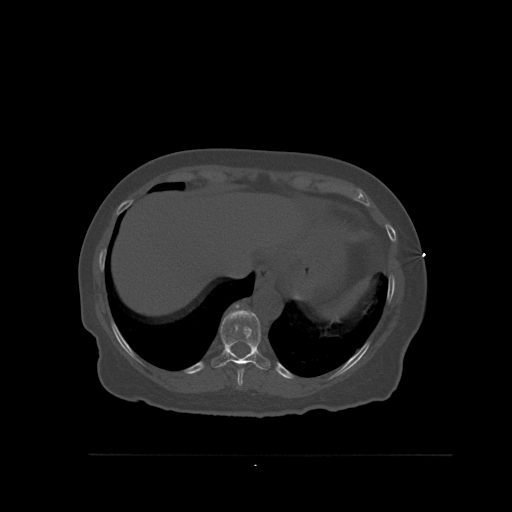
CT including the spine, one axial slice. Slice 321 of 527 in the series (ordered by position). Bone window (W 1800 / L 400 HU). 512 × 512 image matrix, field of view 470 × 470 mm. Female patient, age 73 years. Case-level facts recorded for this patient, not image findings: primary cancer: breast; vertebrae with lytic lesions (as recorded): L2.
Structures marked on this image (semi-automatically segmented with operator editing):
- T10 vertebra: bounding box <211,310,271,370> (left, top, right, bottom; pixels)
- T9 vertebra: <237,364,244,386>